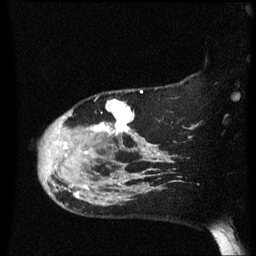
Breast MRI (dynamic contrast-enhanced), one sagittal slice. Slice 49 of 60 in the series (ordered by position). Dynamic contrast-enhanced series, image 2 of 3 at this slice position (ordered by acquisition). 1.5 T. TE 4.2 ms, TR 8.4 ms. 2.2 mm slice thickness. 256 × 256 image matrix, field of view 200 × 200 mm. Patient: female, 47 years.
Annotated regions visible in this slice (semi-automatic segmentation, software-assisted and operator-edited):
- analysis volume of interest (the breast-tissue region the enhancement analysis was run in; not a lesion): bounding box [x1, y1, x2, y2] px = [40, 101, 149, 206]
- tumour enhancement mask (voxels above the 70 % enhancement threshold inside the analysis volume of interest): [66, 101, 143, 199]